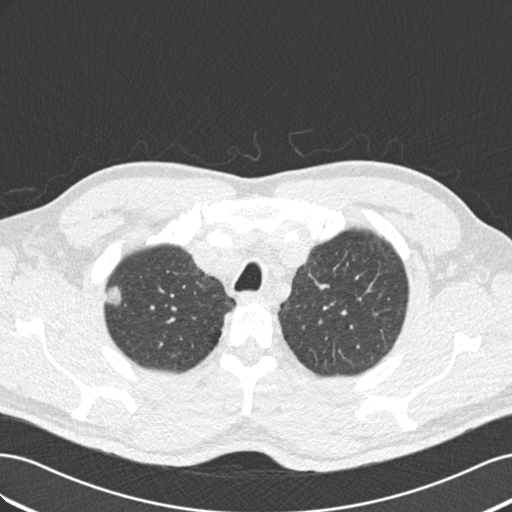
Low-dose screening chest CT, one axial slice; slice 151 of 187 in the series (ordered by position); reconstruction kernel B30f; 120 kVp; lung window (W 1500 / L -600 HU); 2 mm slice thickness; 512 × 512 image matrix, field of view 360 × 360 mm.
Outlined on this slice (outlined manually by an expert reader):
- lesion 1 (tumor, upper lobe of right lung): bounding box [x1, y1, x2, y2] px = [105, 286, 122, 306]